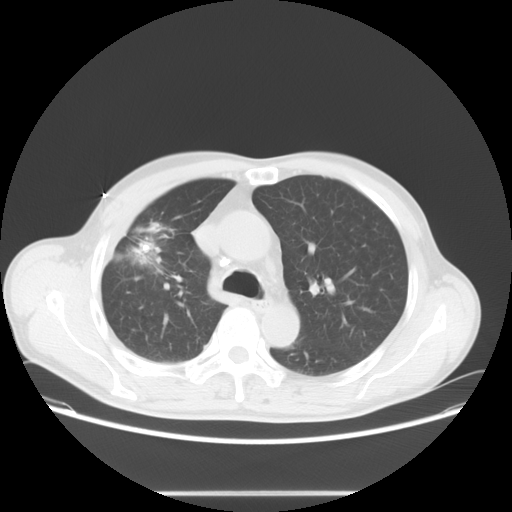
Chest CT, one axial slice. Position 48 of 71 along the scan axis. Reconstruction kernel STANDARD. Lung window (W 1500 / L -600 HU). 5 mm slice thickness. 512 × 512 image matrix, field of view 392 × 392 mm. Patient: male, 67 years. From the clinical record (not read from this slice): clinical TNM (as recorded): T2 N0 M0.
Structures marked on this image (rectangle marked by the reading radiologist):
- lung tumour (recorded histology: adenocarcinoma): bounding box (x1, y1, x2, y2) in pixels: (135, 239, 162, 256)